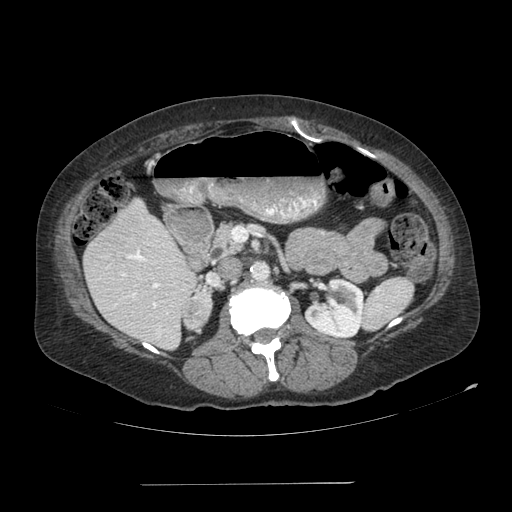
Contrast-enhanced abdominal CT, one axial slice. Slice 50 of 113 in the series (ordered by position). Reconstruction kernel SOFT. Soft-tissue window (W 400 / L 40 HU). 2.5 mm slice thickness. 512 × 512 image matrix, field of view 440 × 440 mm. Female patient, age 67 years. Case-level facts recorded for this patient, not image findings: diagnosis: adrenocortical carcinoma; tumour side: right adrenal; tumour size at pathology: 9.8 cm; Ki-67 index: 59 %; stage (as recorded): 4.
Outlined on this slice (semi-automatic segmentation, software-assisted and operator-edited):
- mass: bounding box <183,294,211,328> (left, top, right, bottom; pixels)